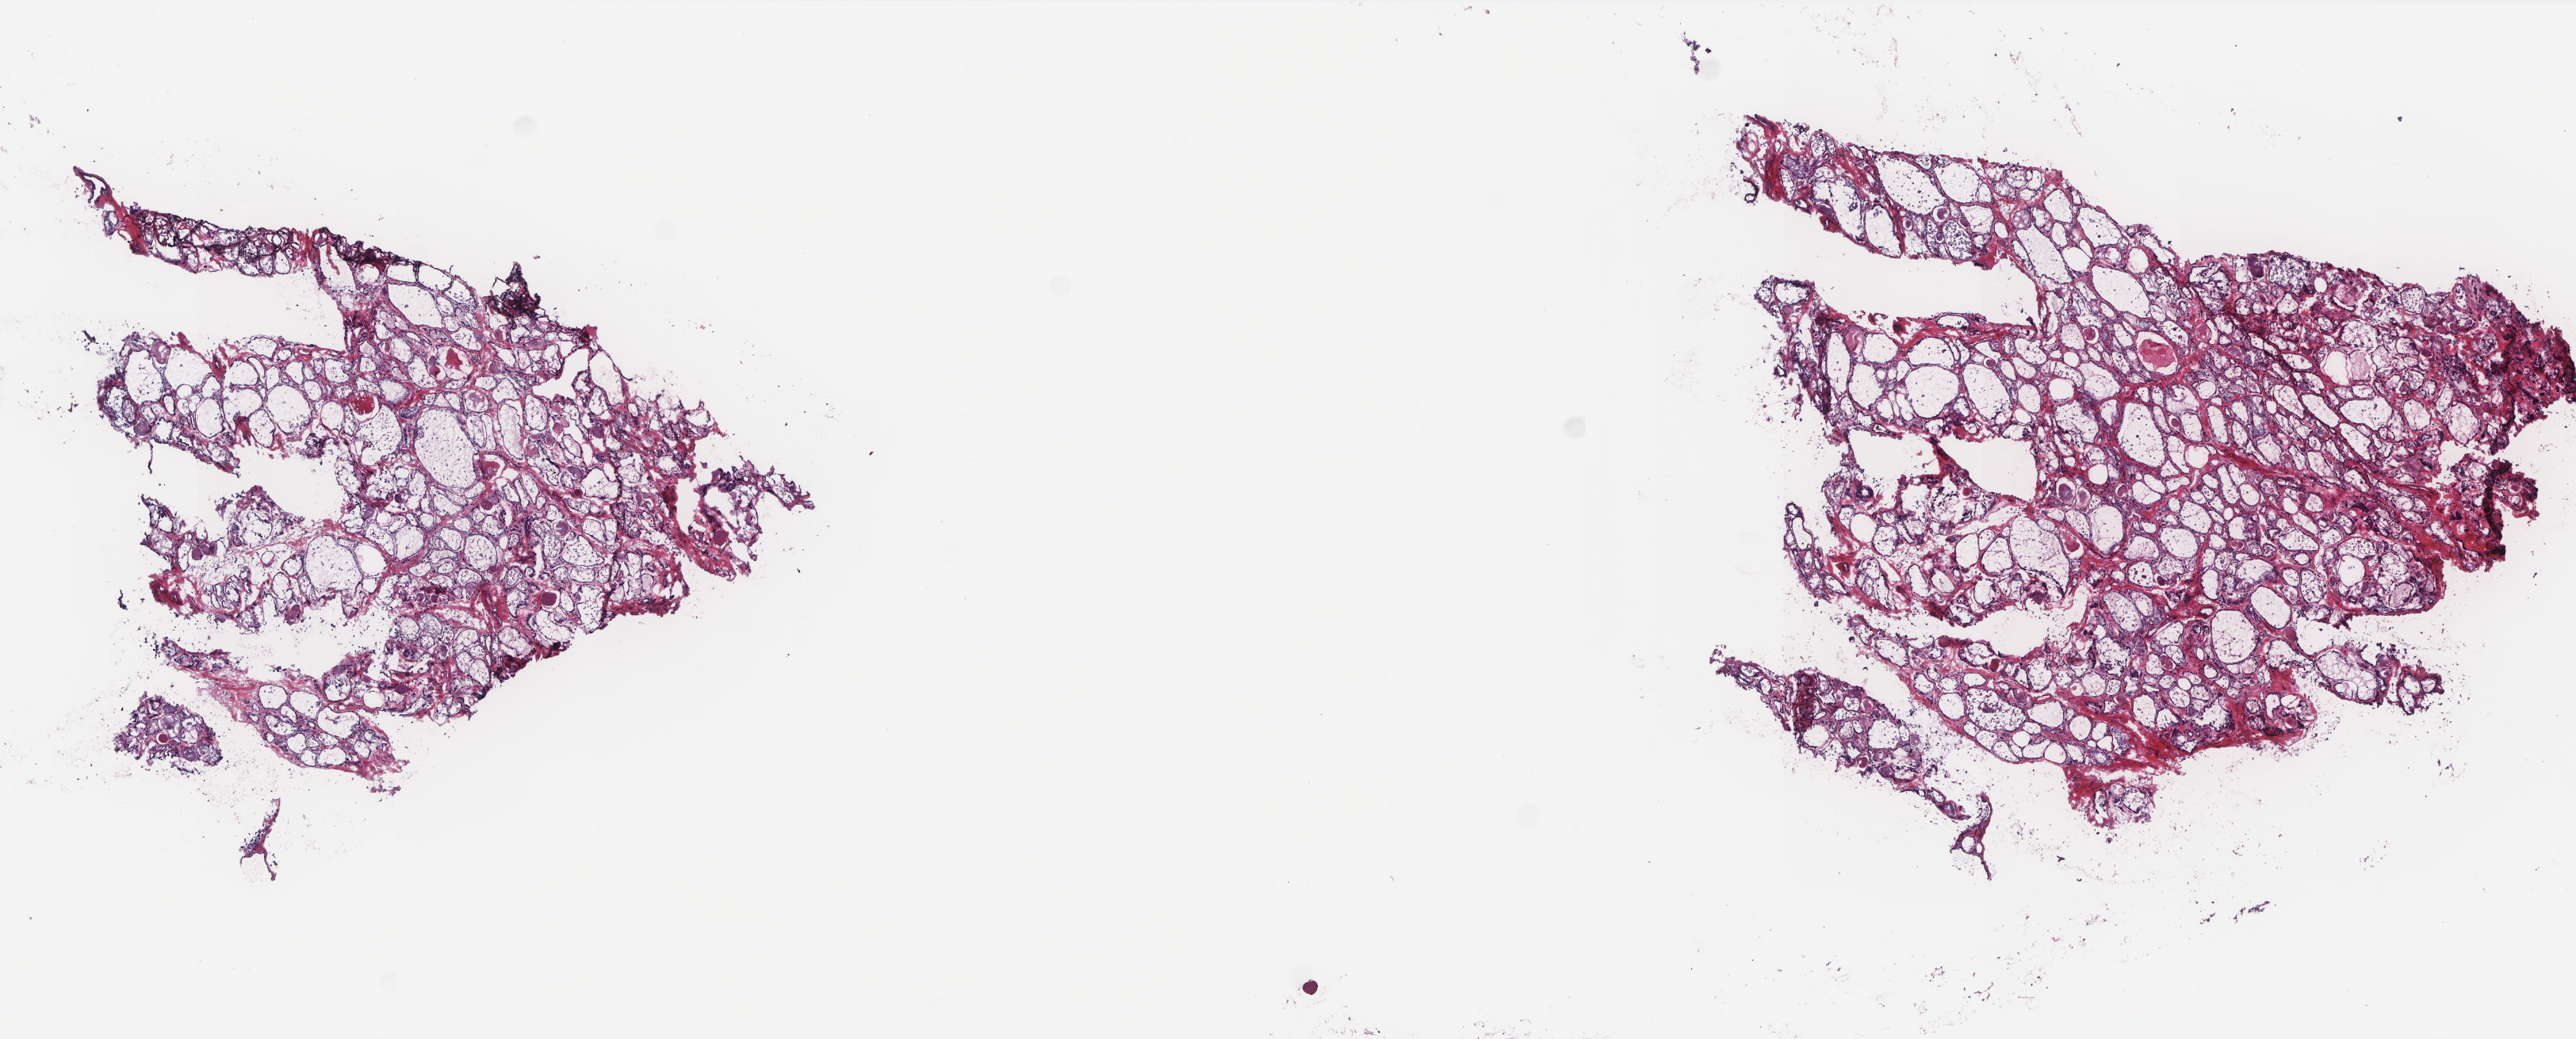
H&E whole-slide image — whole scanned area (about 13.0 x 5.2 mm, acquisition: 20x scan) shown as a low-resolution overview. Frozen section. Solid tissue normal (non-tumour tissue) sample from the thyroid. Male patient; age at initial diagnosis 64 years. Slide review estimates, as recorded: tumour cells 0%, tumour nuclei 0%.
This section: solid tissue normal sample (biorepository sample class). Patient diagnosis: Papillary carcinoma, columnar cell.